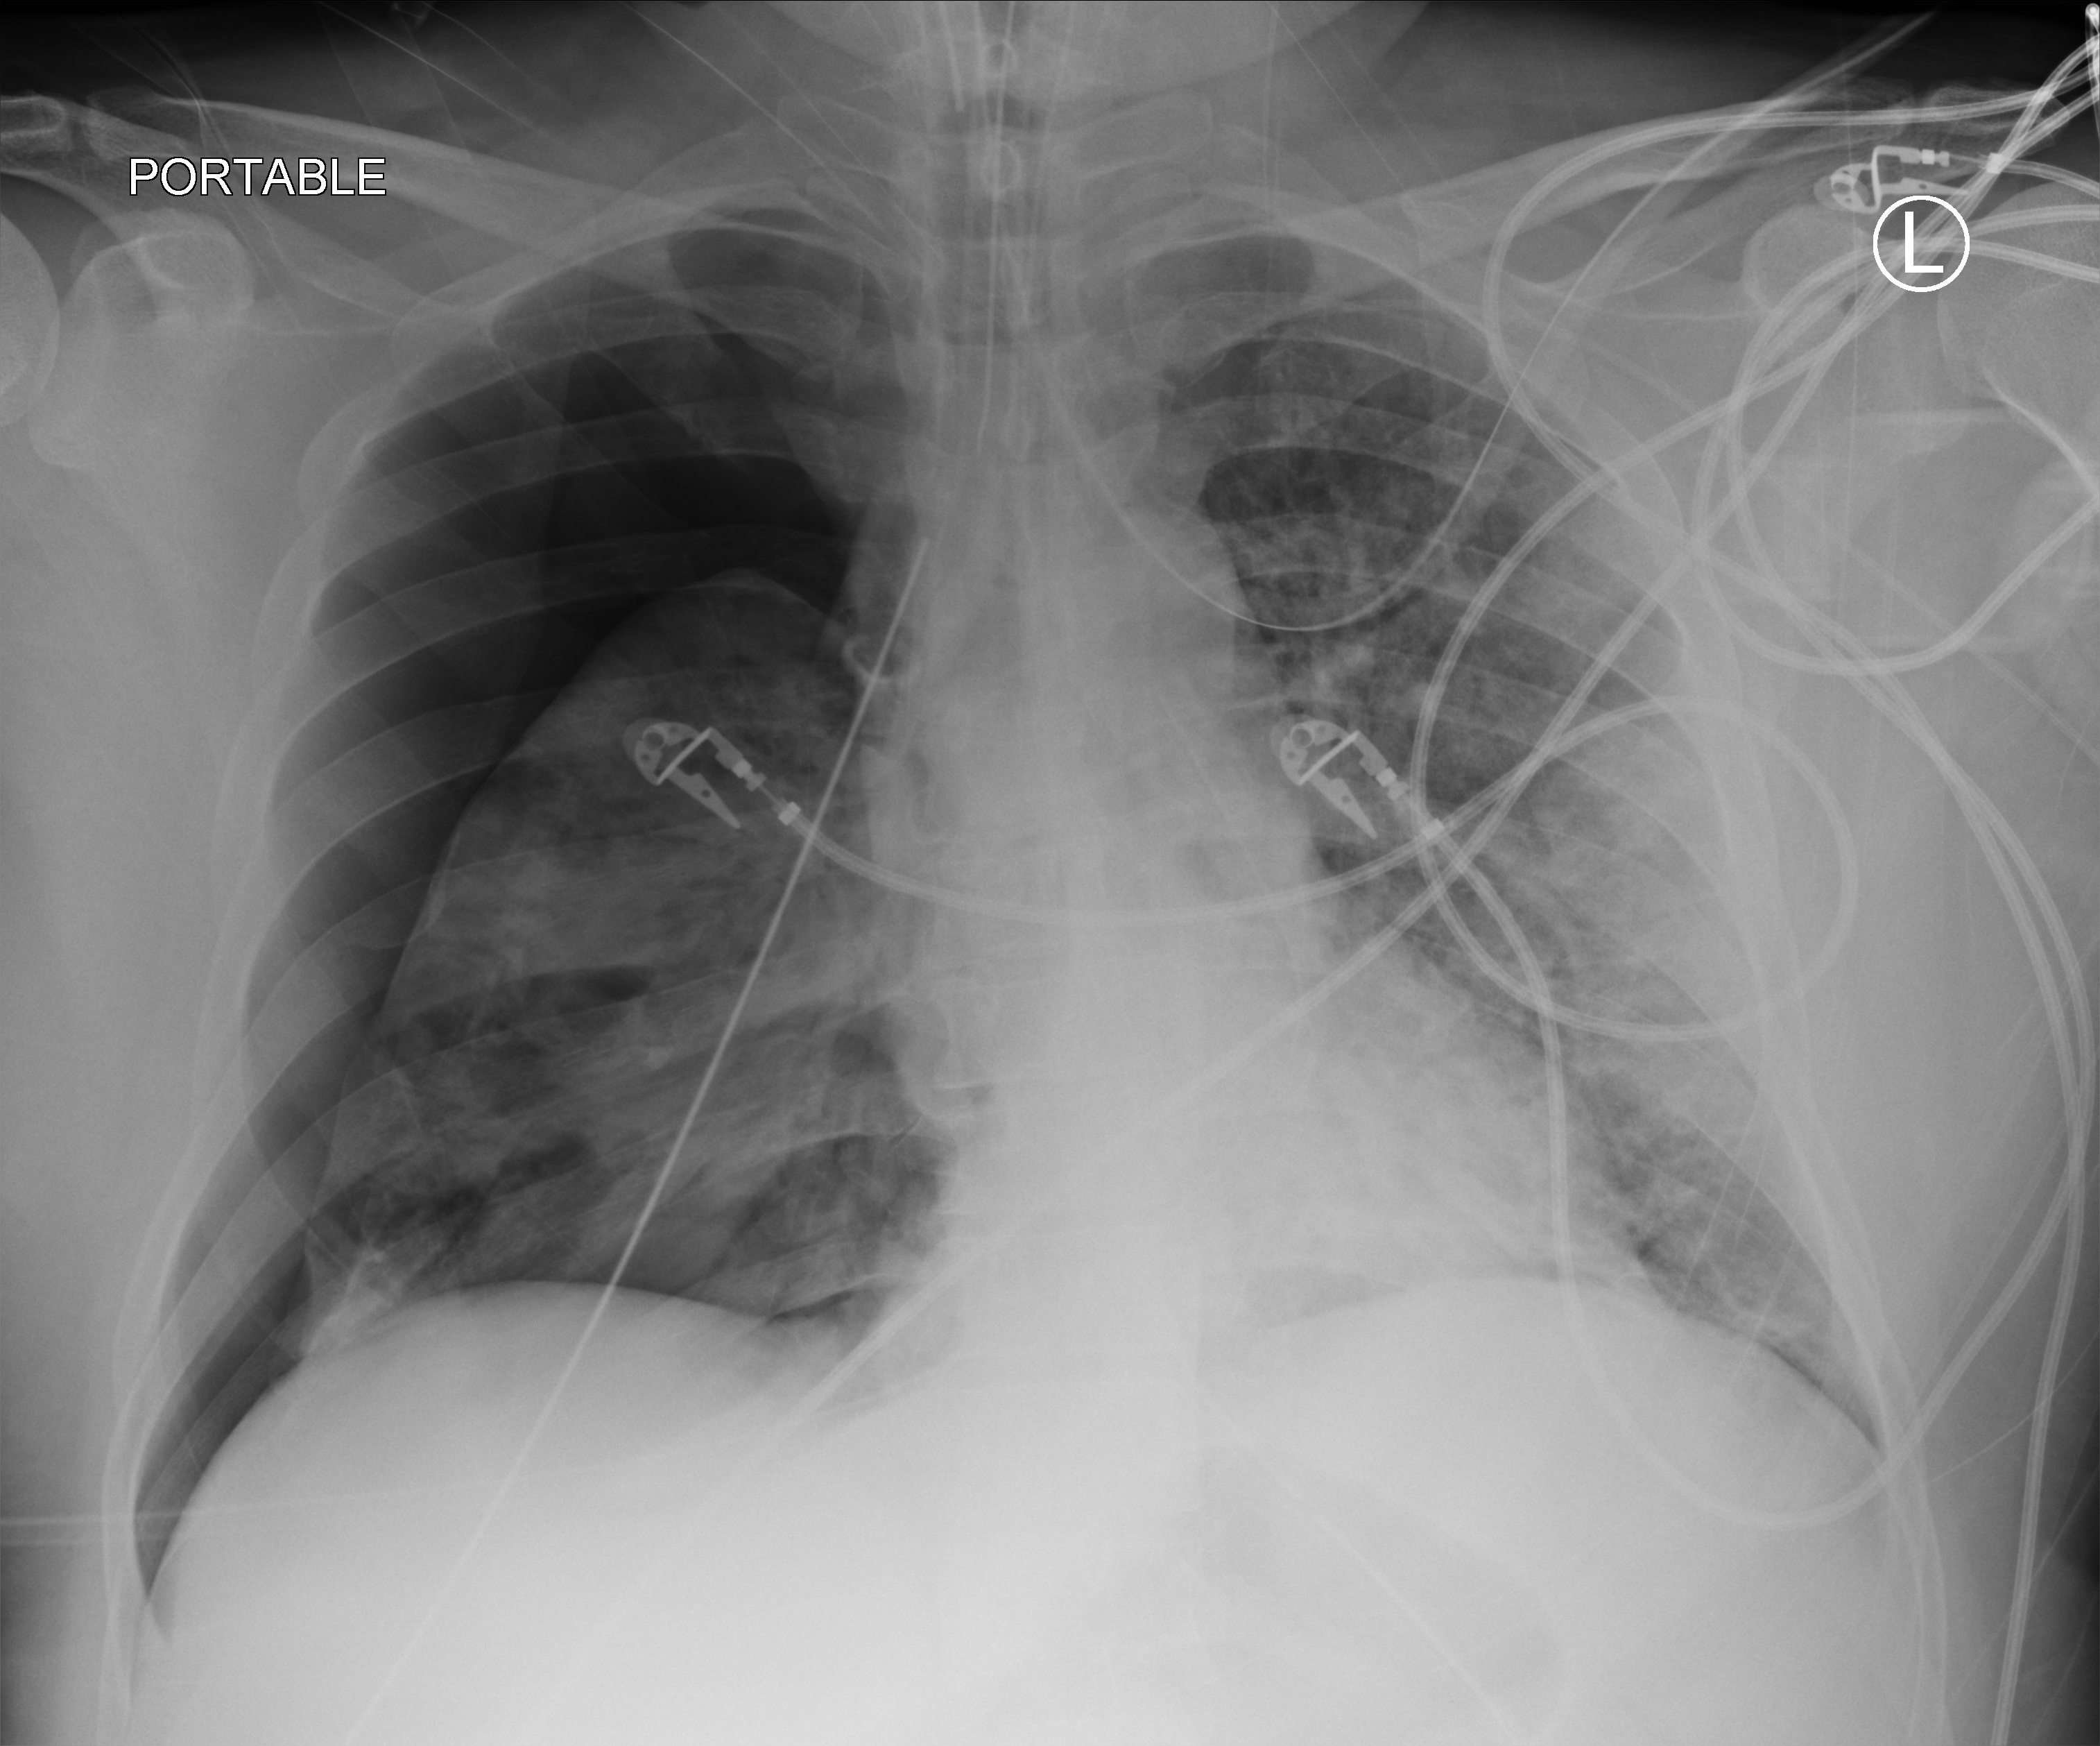
Chest X-ray (portable), anteroposterior (AP) projection. Patient hospitalised with COVID-19; male, aged 18–59 years.
Admission-level facts for this patient (not findings on this image; timing relative to this image not recorded): chronic kidney disease (admission record): no; length of hospital stay: 63 days; COPD (admission record): no.